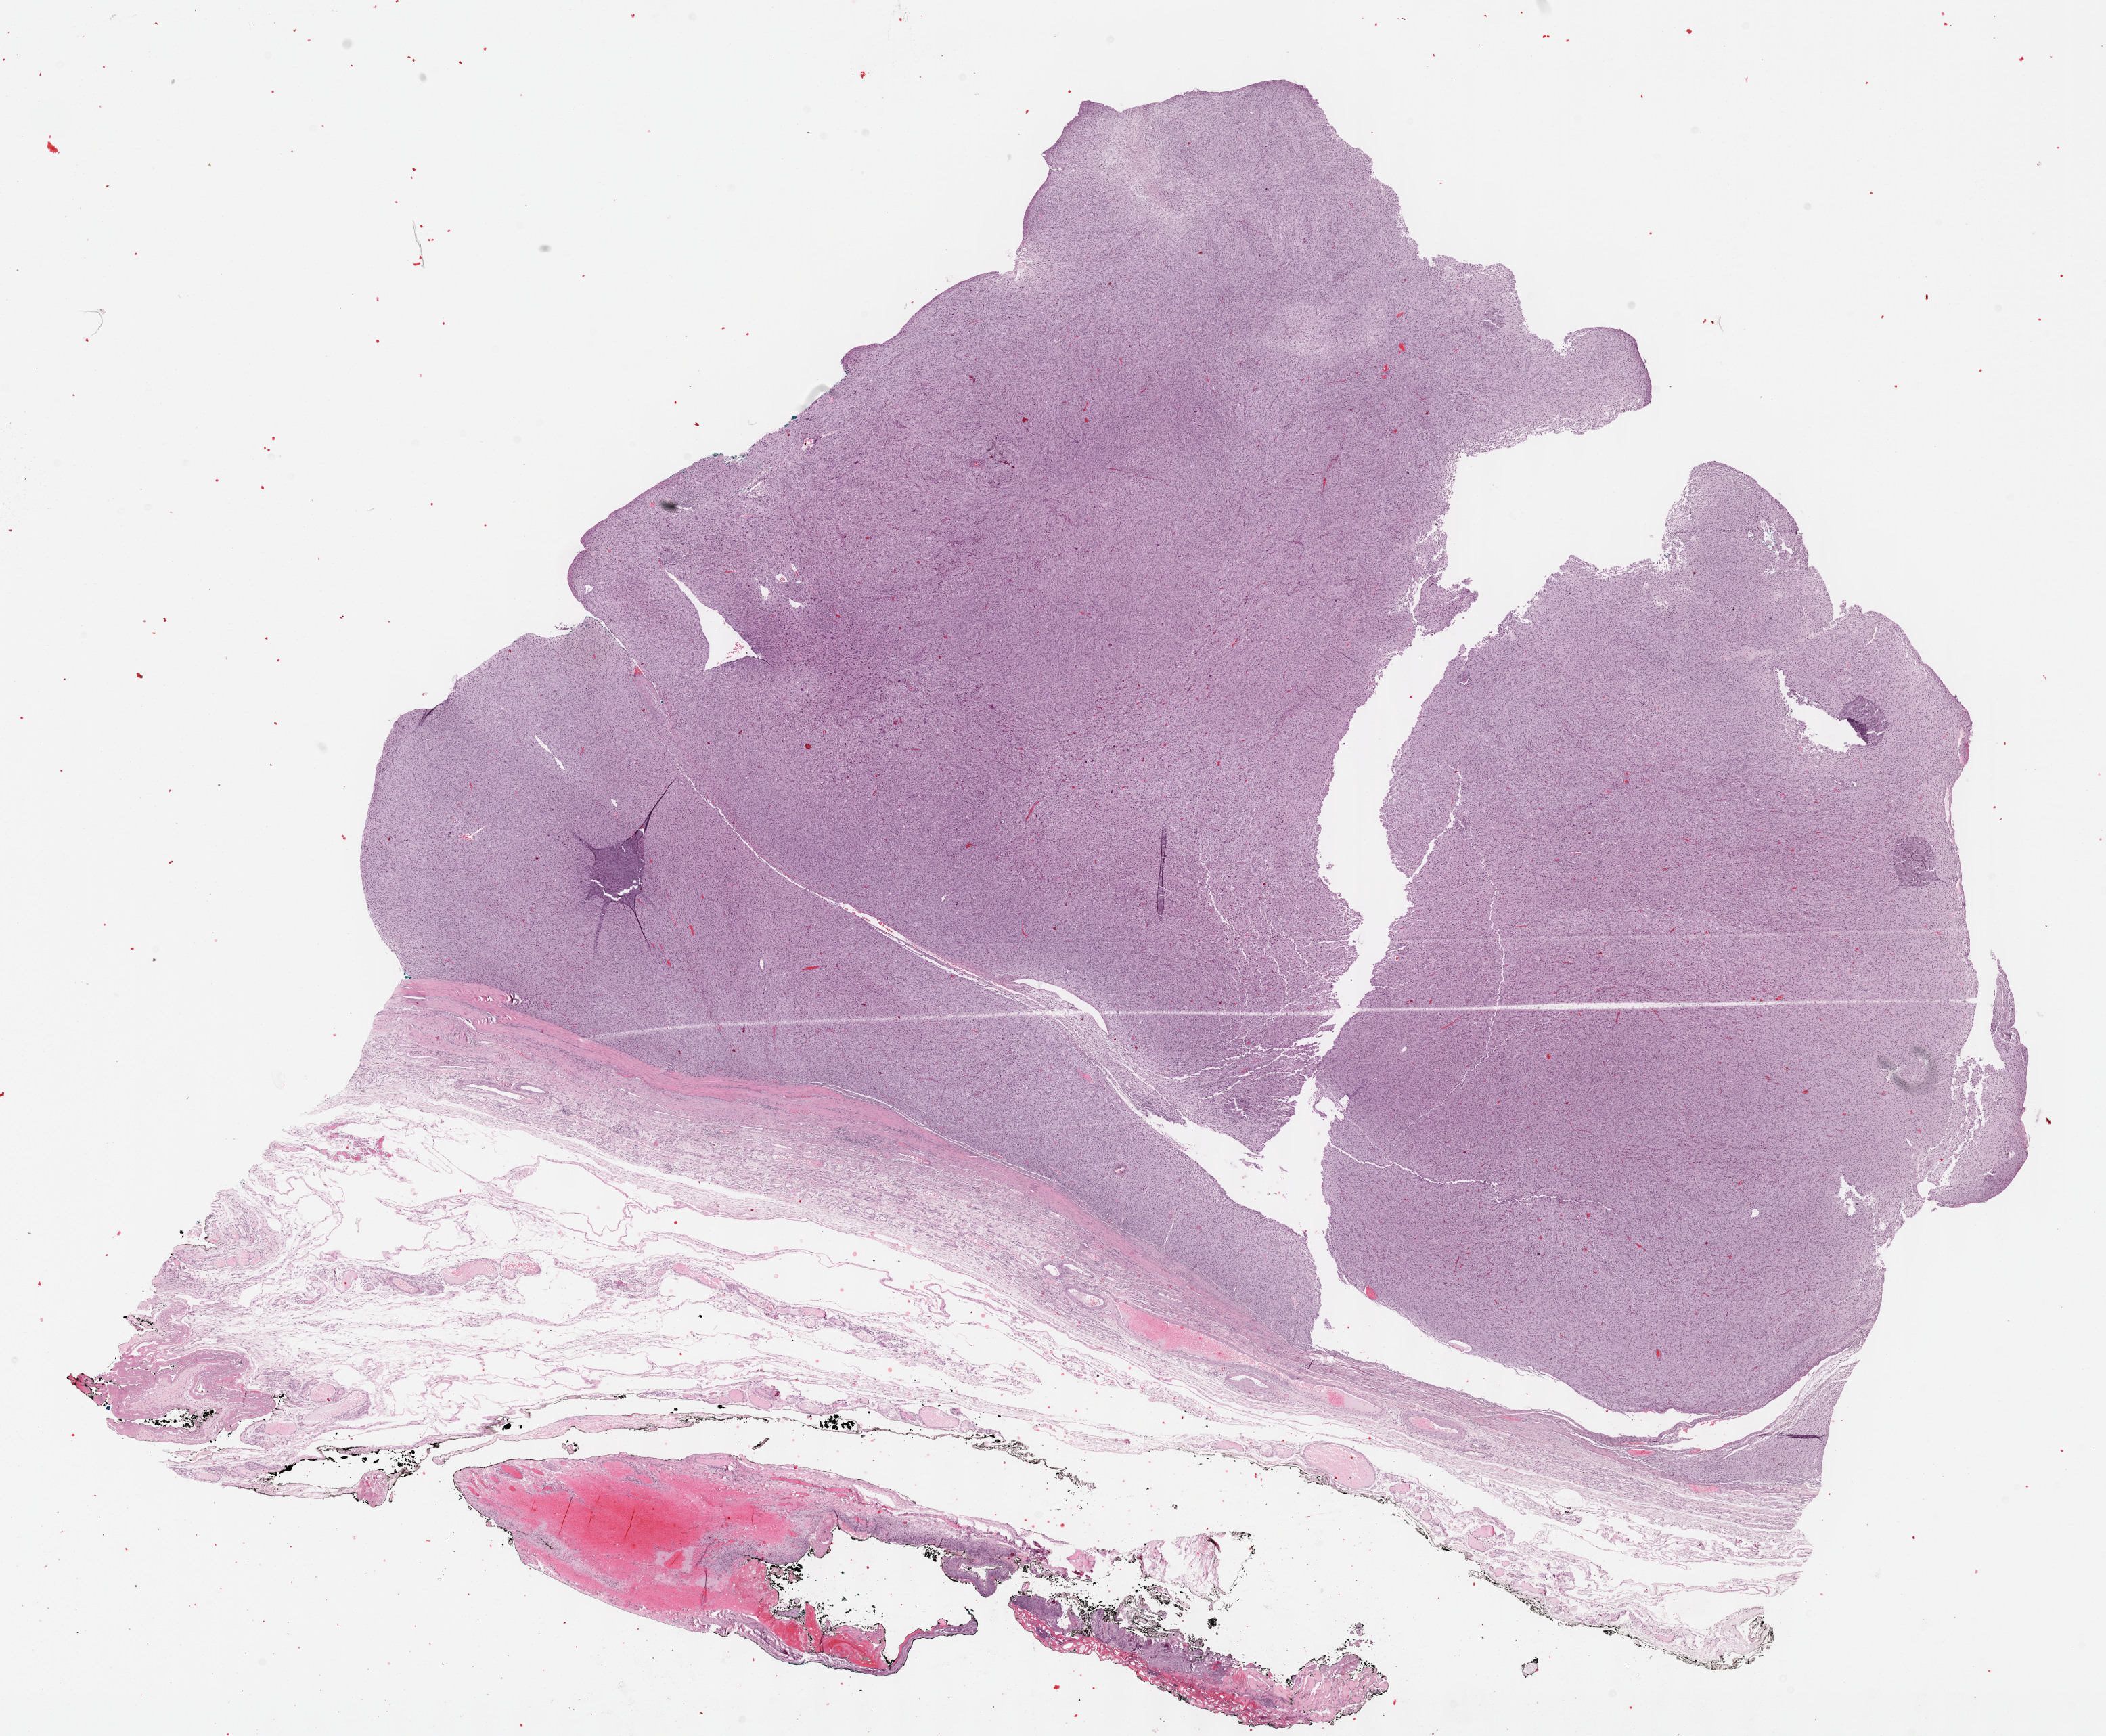
Whole-slide histology image, Hematoxylin and eosin (H&E) stained, shown as a low-resolution overview of the whole scanned area (about 25.1 x 20.7 mm, slide scanned at 40x), formalin-fixed paraffin-embedded (FFPE) diagnostic section, sample: primary tumour, connective, subcutaneous and other soft tissues. Patient: male, age at initial diagnosis 60 years.
Histologic diagnosis: Undifferentiated sarcoma (connective, subcutaneous and other soft tissues of lower limb and hip).